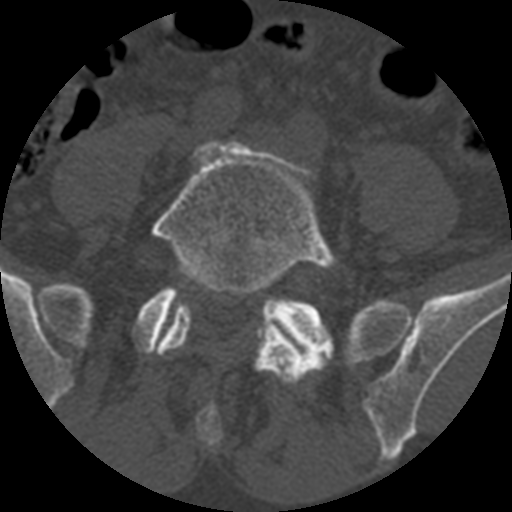
CT including the spine, one axial slice; position 251 of 399 along the scan axis; 120 kVp; bone window (W 1800 / L 400 HU); 1.25 mm slice thickness; 512 × 512 image matrix, field of view 160 × 160 mm. Patient age 71 years. Case-level facts recorded for this patient, not image findings: primary cancer: prostate.
Annotated regions visible in this slice (semi-automatically segmented with operator editing):
- L5 vertebra: bounding box <149,142,339,385> (left, top, right, bottom; pixels)